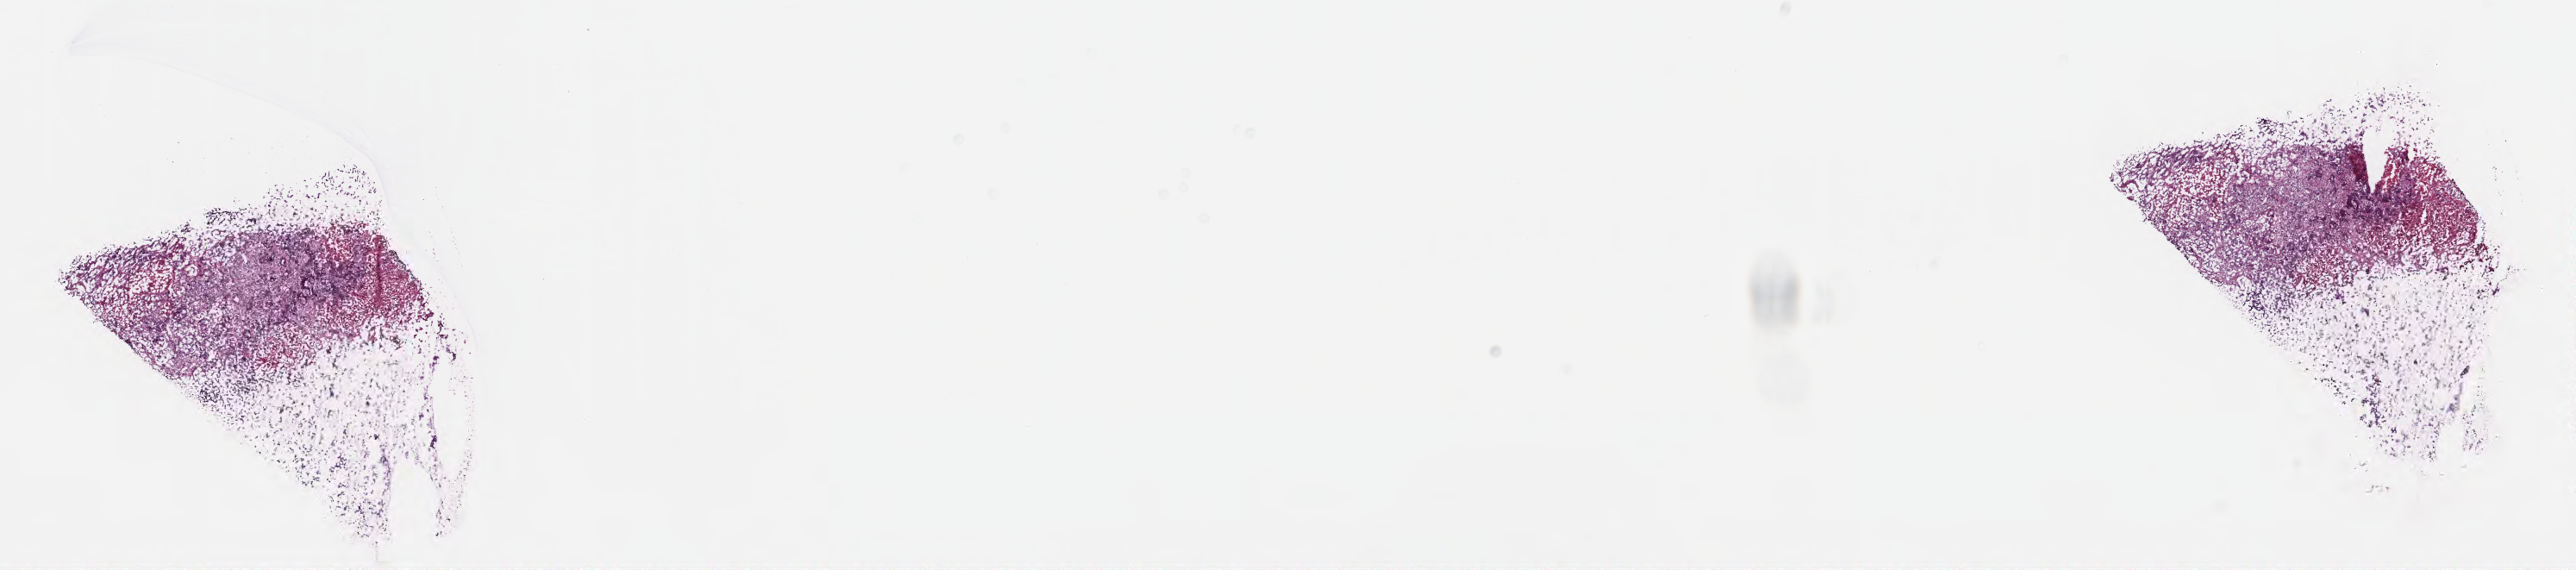
Whole-slide image, haematoxylin and eosin stain, shown as a low-resolution overview of the whole scanned area (about 24.1 x 5.3 mm); frozen section; metastatic tumor tissue, resected from liver. Male patient; age at initial diagnosis 59 years. Slide review estimates, as recorded: tumor cells 50%, tumor nuclei 70%, stromal cells 50%, necrosis 0%, normal cells 0%. Inflammatory infiltration, as recorded: lymphocyte infiltration 0%, monocyte infiltration 0%, neutrophil infiltration 0%.
Patient diagnosis (primary): Adenocarcinoma, metastatic, NOS.